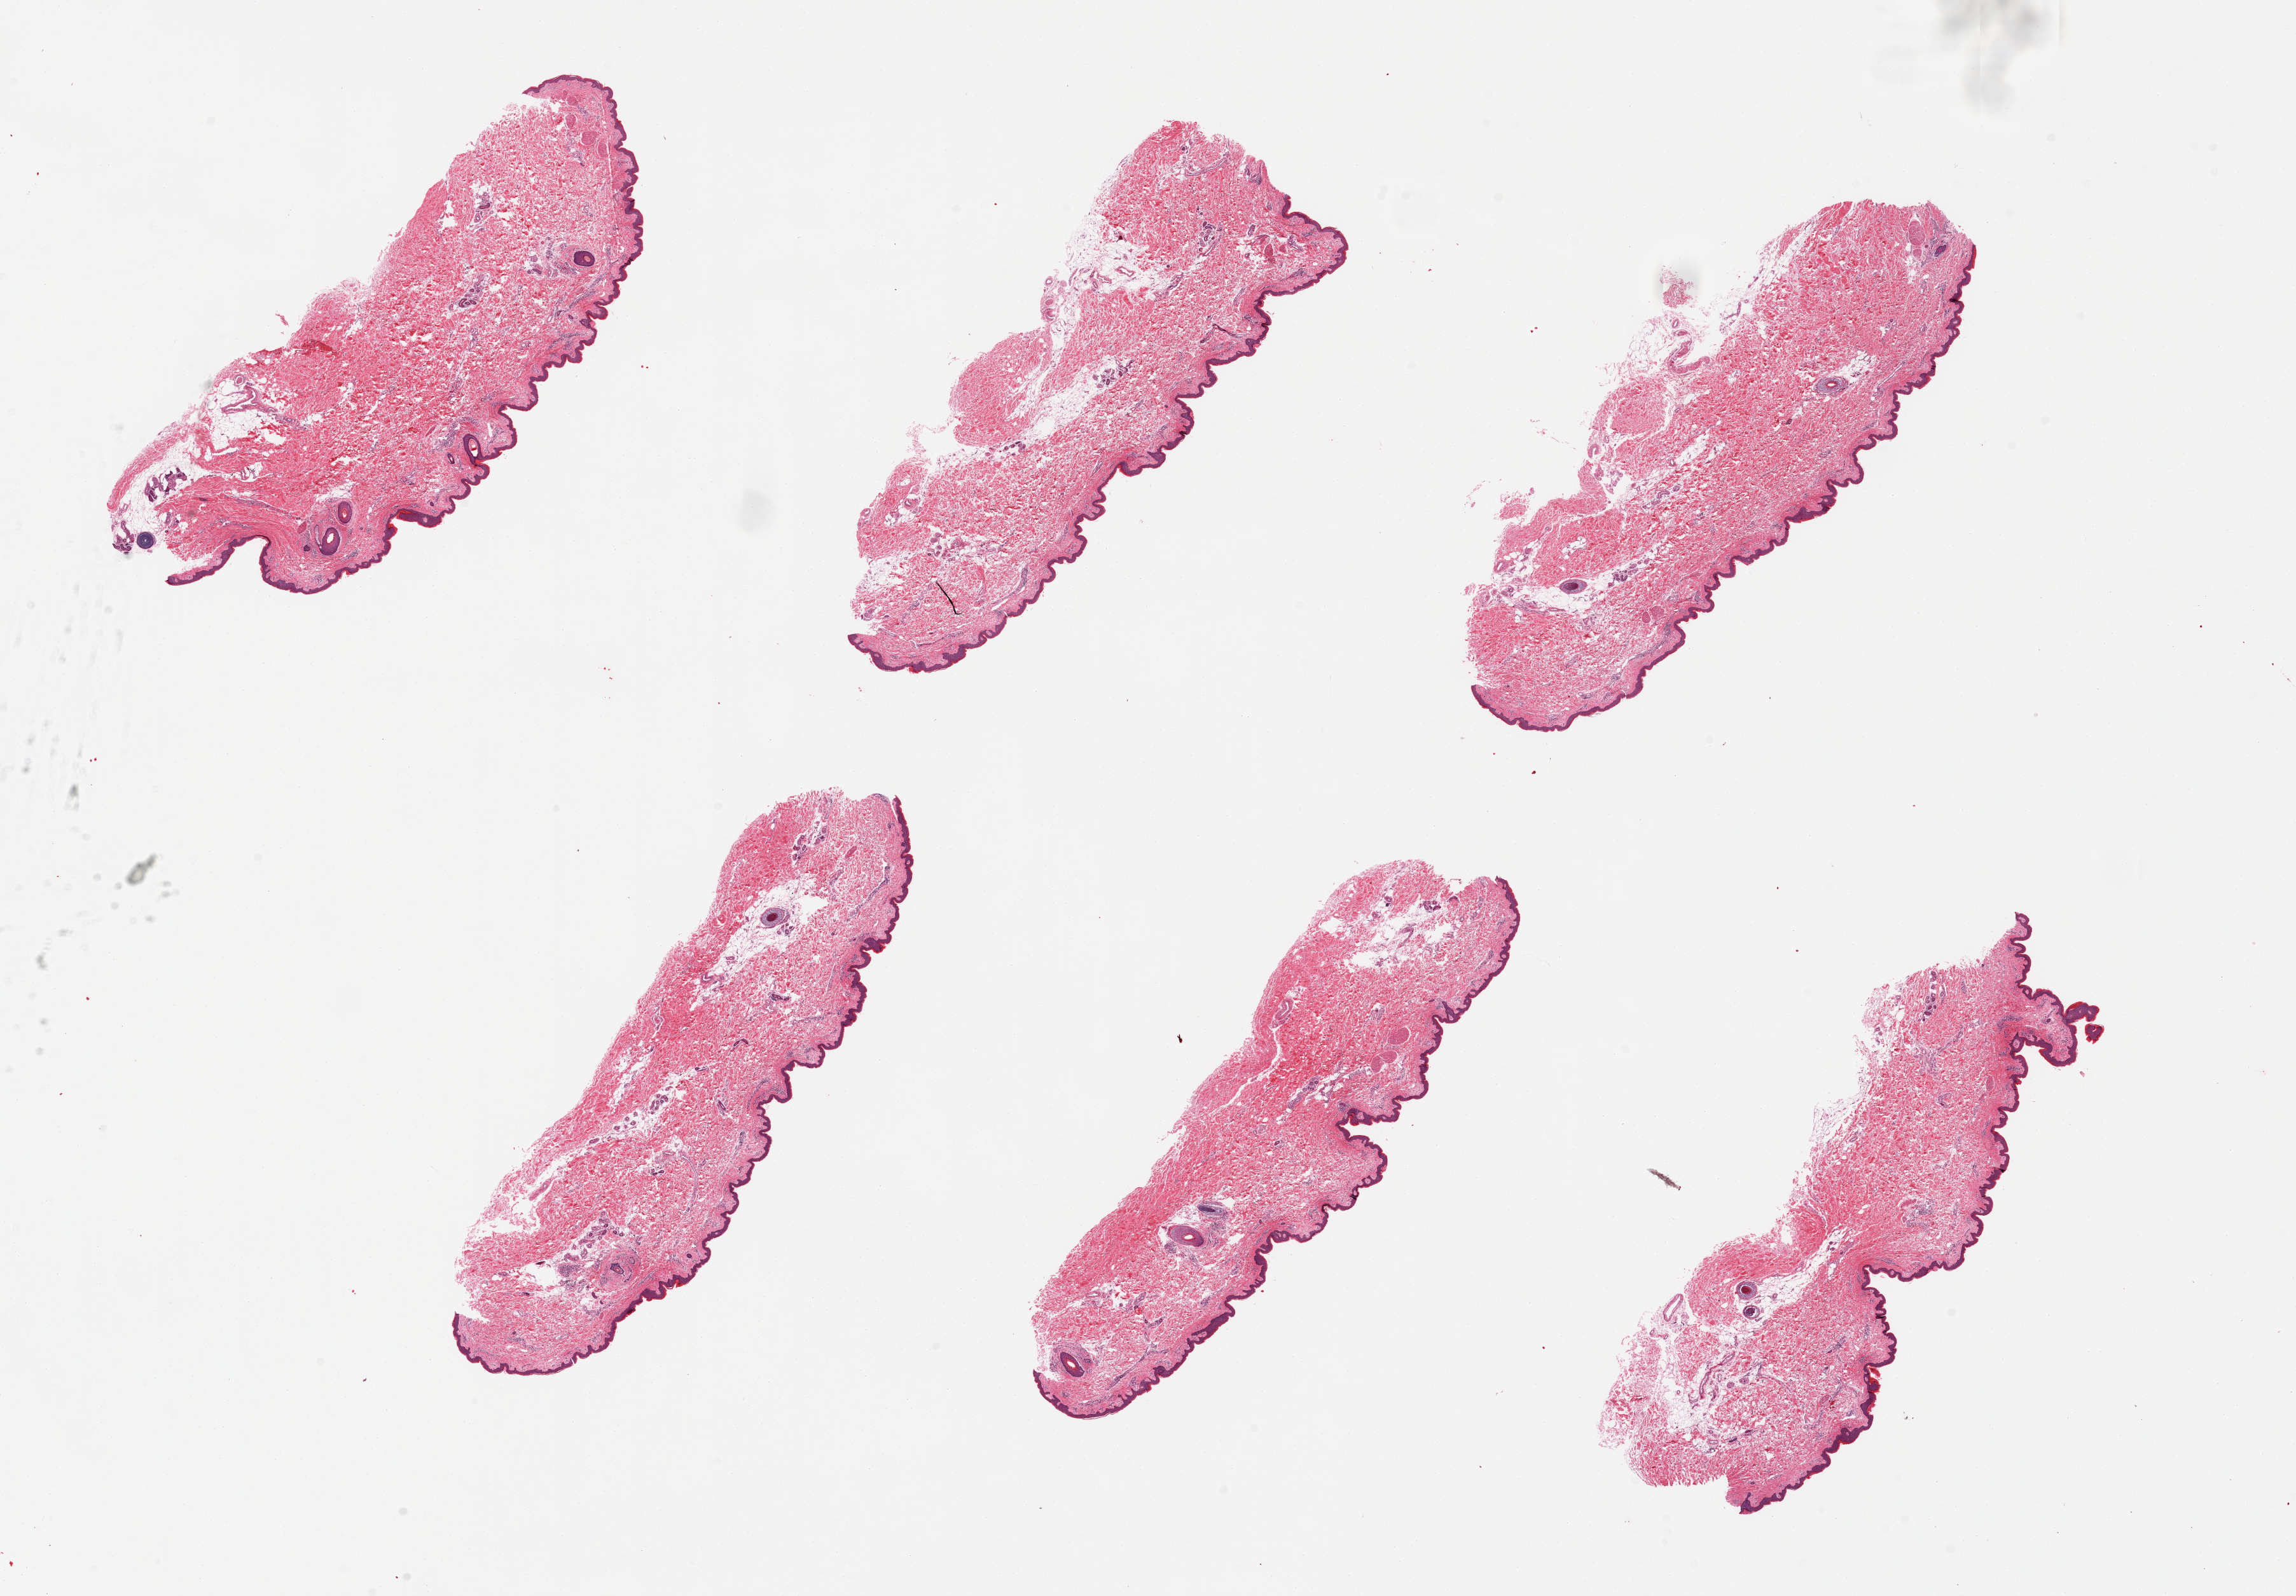
Whole-slide image, hematoxylin and eosin (H&E) stain, brightfield — a low-resolution overview of the entire scanned area, about 28.5 x 19.8 mm; PAXgene-fixed paraffin-embedded (PFPE) section; sampled site (target tissue): skin of lower leg; donor tissue sample. Donor: male.
Reviewer comment on this tissue sample: 6 pieces; well trimmed; 10% intradermal fat.